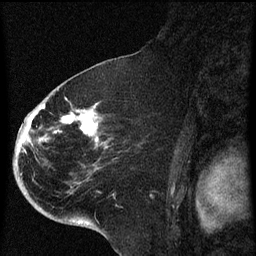
Breast MRI (dynamic contrast-enhanced), one sagittal slice; slice 38 of 60 in the series (ordered by position); dynamic contrast-enhanced series, image 2 of 4 at this slice position (ordered by acquisition); 1.5 T; TE 4.2 ms, TR 8 ms; 256 × 256 image matrix, field of view 180 × 180 mm. Patient: female, 71 years.
Structures marked on this image (semi-automatically segmented with operator editing):
- analysis volume of interest (the breast-tissue region the enhancement analysis was run in; not a lesion): bounding box <32,86,140,205> (left, top, right, bottom; pixels)
- tumour enhancement mask (voxels above the 70 % enhancement threshold inside the analysis volume of interest): <39,98,98,147>